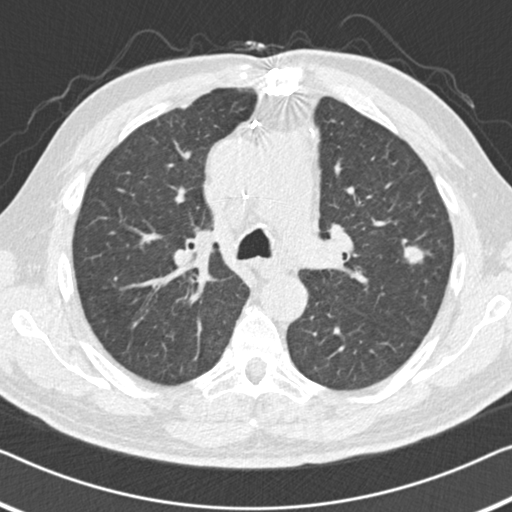
Low-dose screening chest CT, axial slice; first (baseline) screen; lung window (W 1500 / L -600 HU); 2 mm slice thickness; 120 kVp; slice 53 of 155 in the series. Male participant, aged 64 years at enrolment. Current smoker at enrolment.
Expert reader's lesion annotation, bounding box (x1, y1, x2, y2) in pixels: (385, 229, 441, 280). The screening reader recorded 2 non-calcified nodules or masses ≥4 mm on this exam (left upper lobe, right middle lobe); which of them this box marks is not recorded. Official screen result: positive, change unspecified: nodule(s) >= 4 mm or enlarging nodule(s), mass(es), or other non-specific abnormalities suspicious for lung cancer. Lung cancer was diagnosed 133 days after this screen: adenocarcinoma, NOS, left upper lobe, poorly differentiated (G3), stage IA (AJCC 6th edition), 15 mm at pathology.